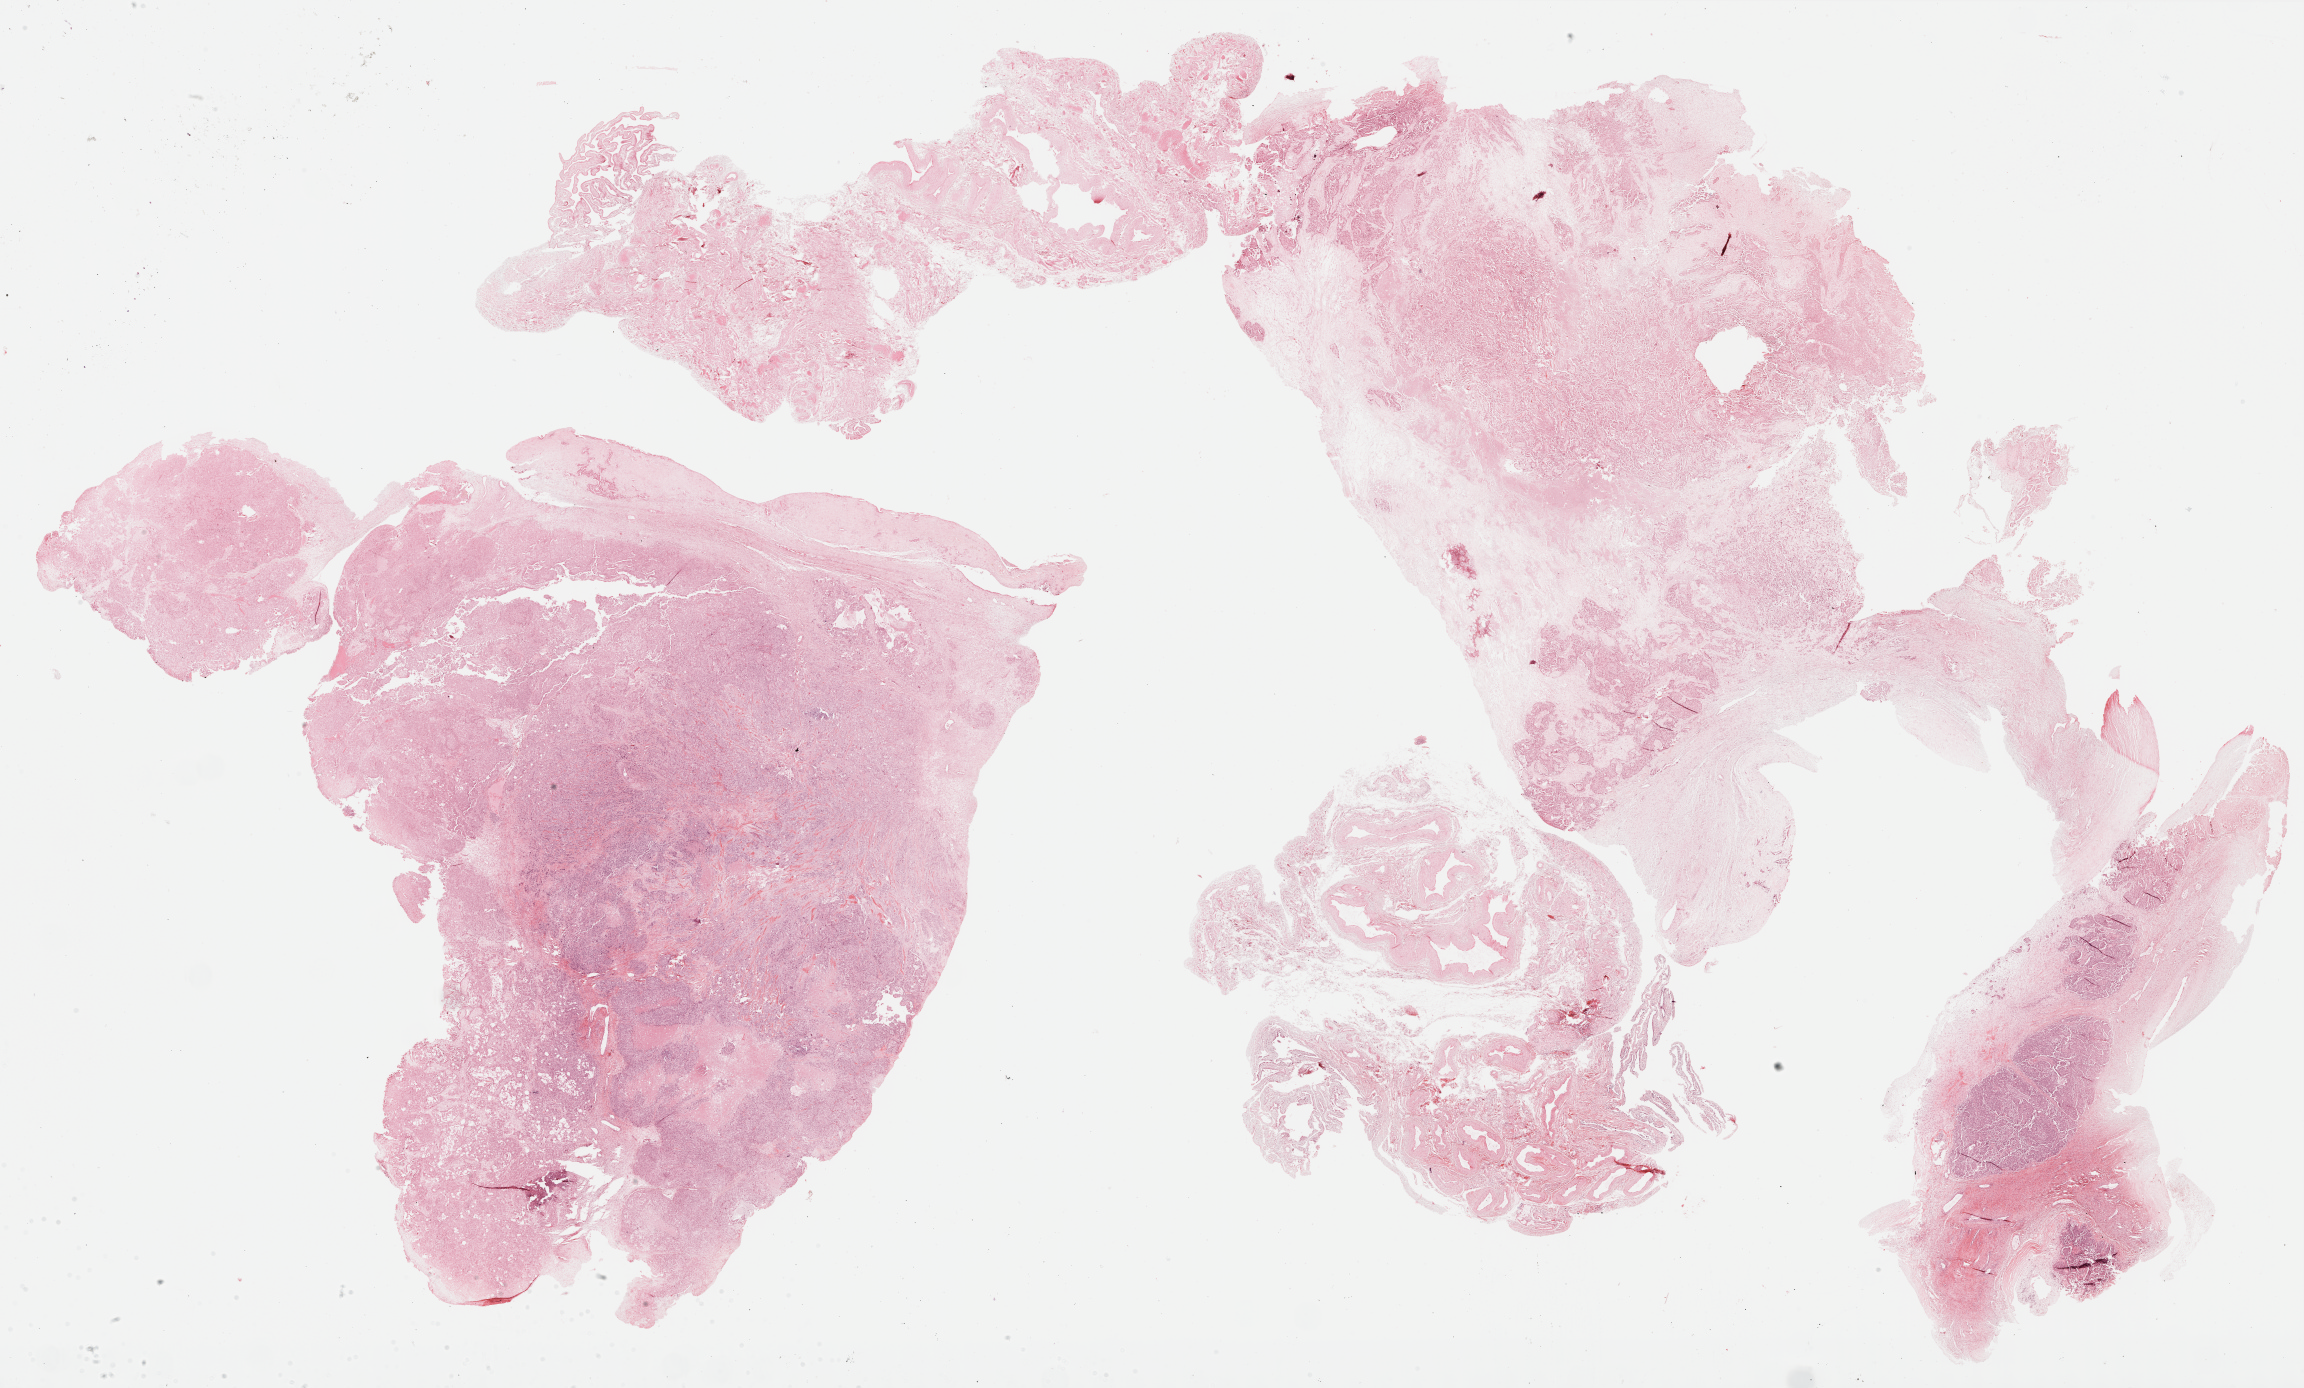
Digitized H&E tissue section (whole slide), low-resolution overview of the scanned area, about 37.2 x 22.4 mm; formalin-fixed paraffin-embedded (FFPE) diagnostic section; sample: primary tumour, ovary. Female, age 54 years at initial diagnosis. Histologic grade: G3 (poorly differentiated).
Histologic diagnosis: Serous cystadenocarcinoma, NOS. FIGO stage: IIIC.